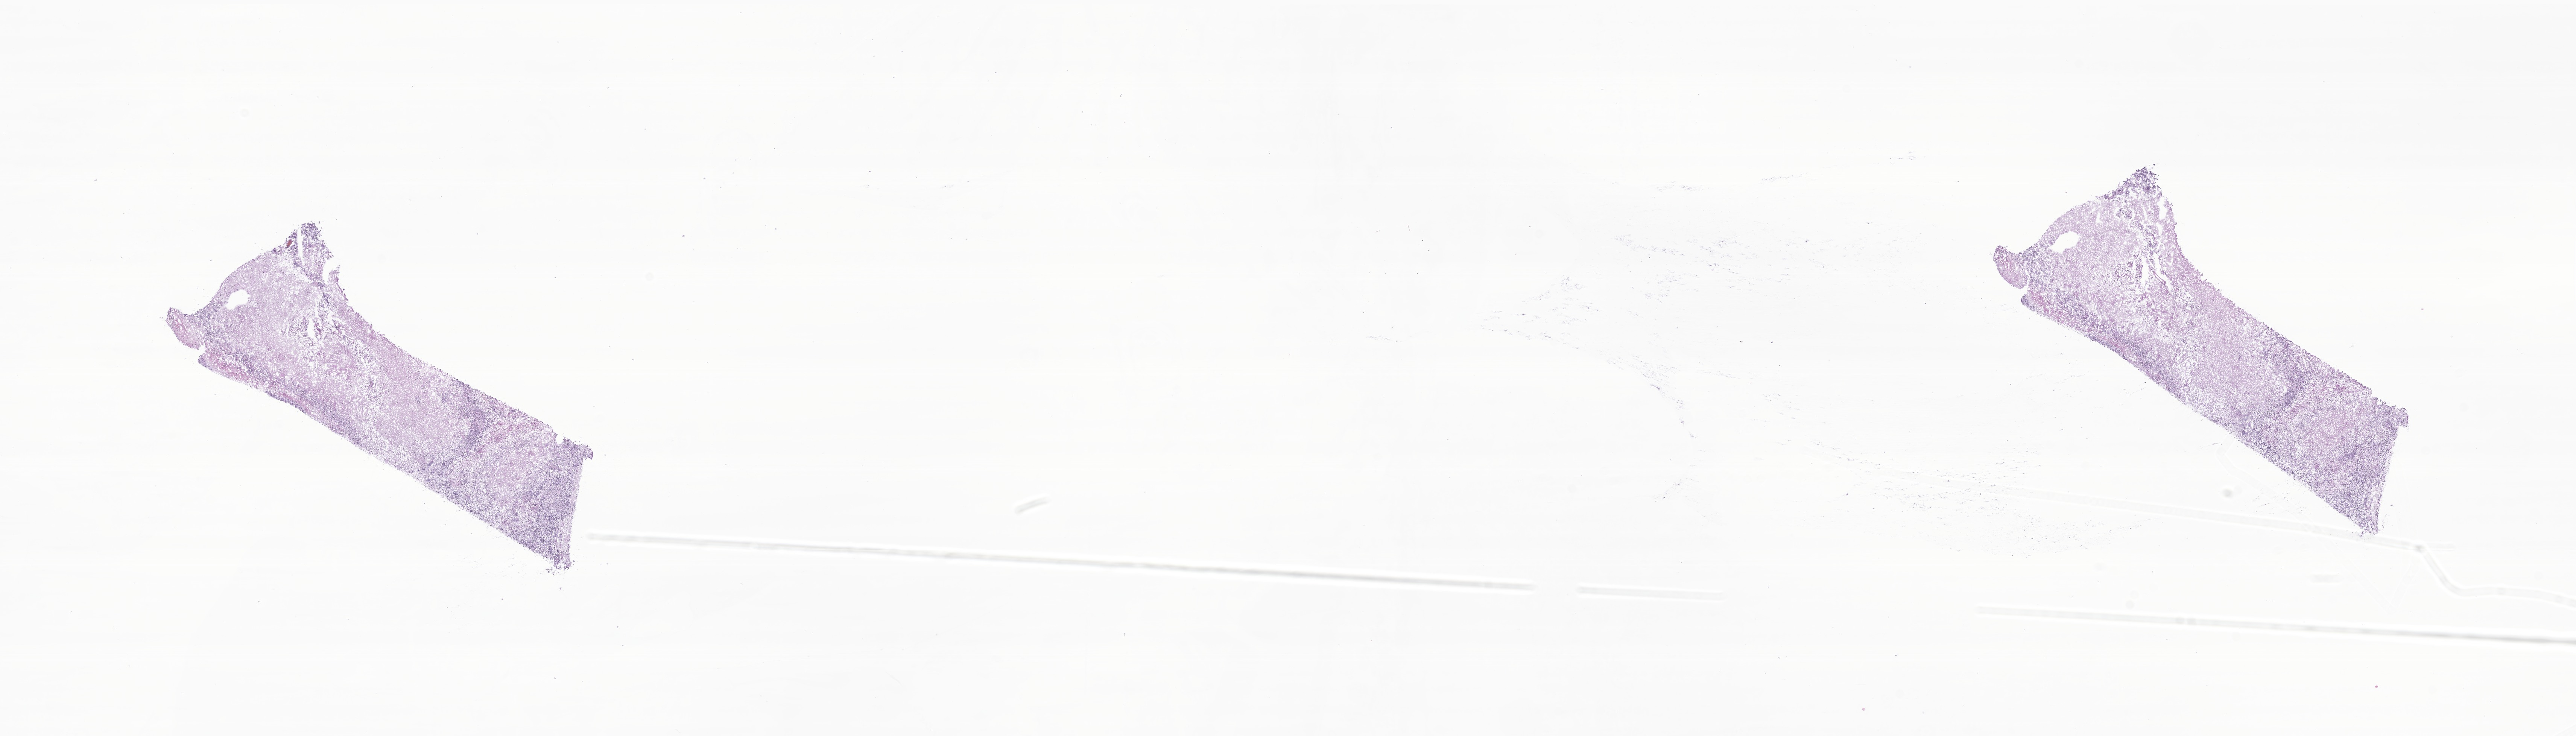
Digitized H&E-stained section of tumor tissue from the cerebral ventricle — shown as a low-resolution overview of the whole scanned area (about 28.9 x 8.2 mm), frozen section (OCT-embedded). Patient: female, age 93 months (7 years 9 months).
Diagnosis (ICD-O-3 morphology term): Medulloblastoma, NOS.